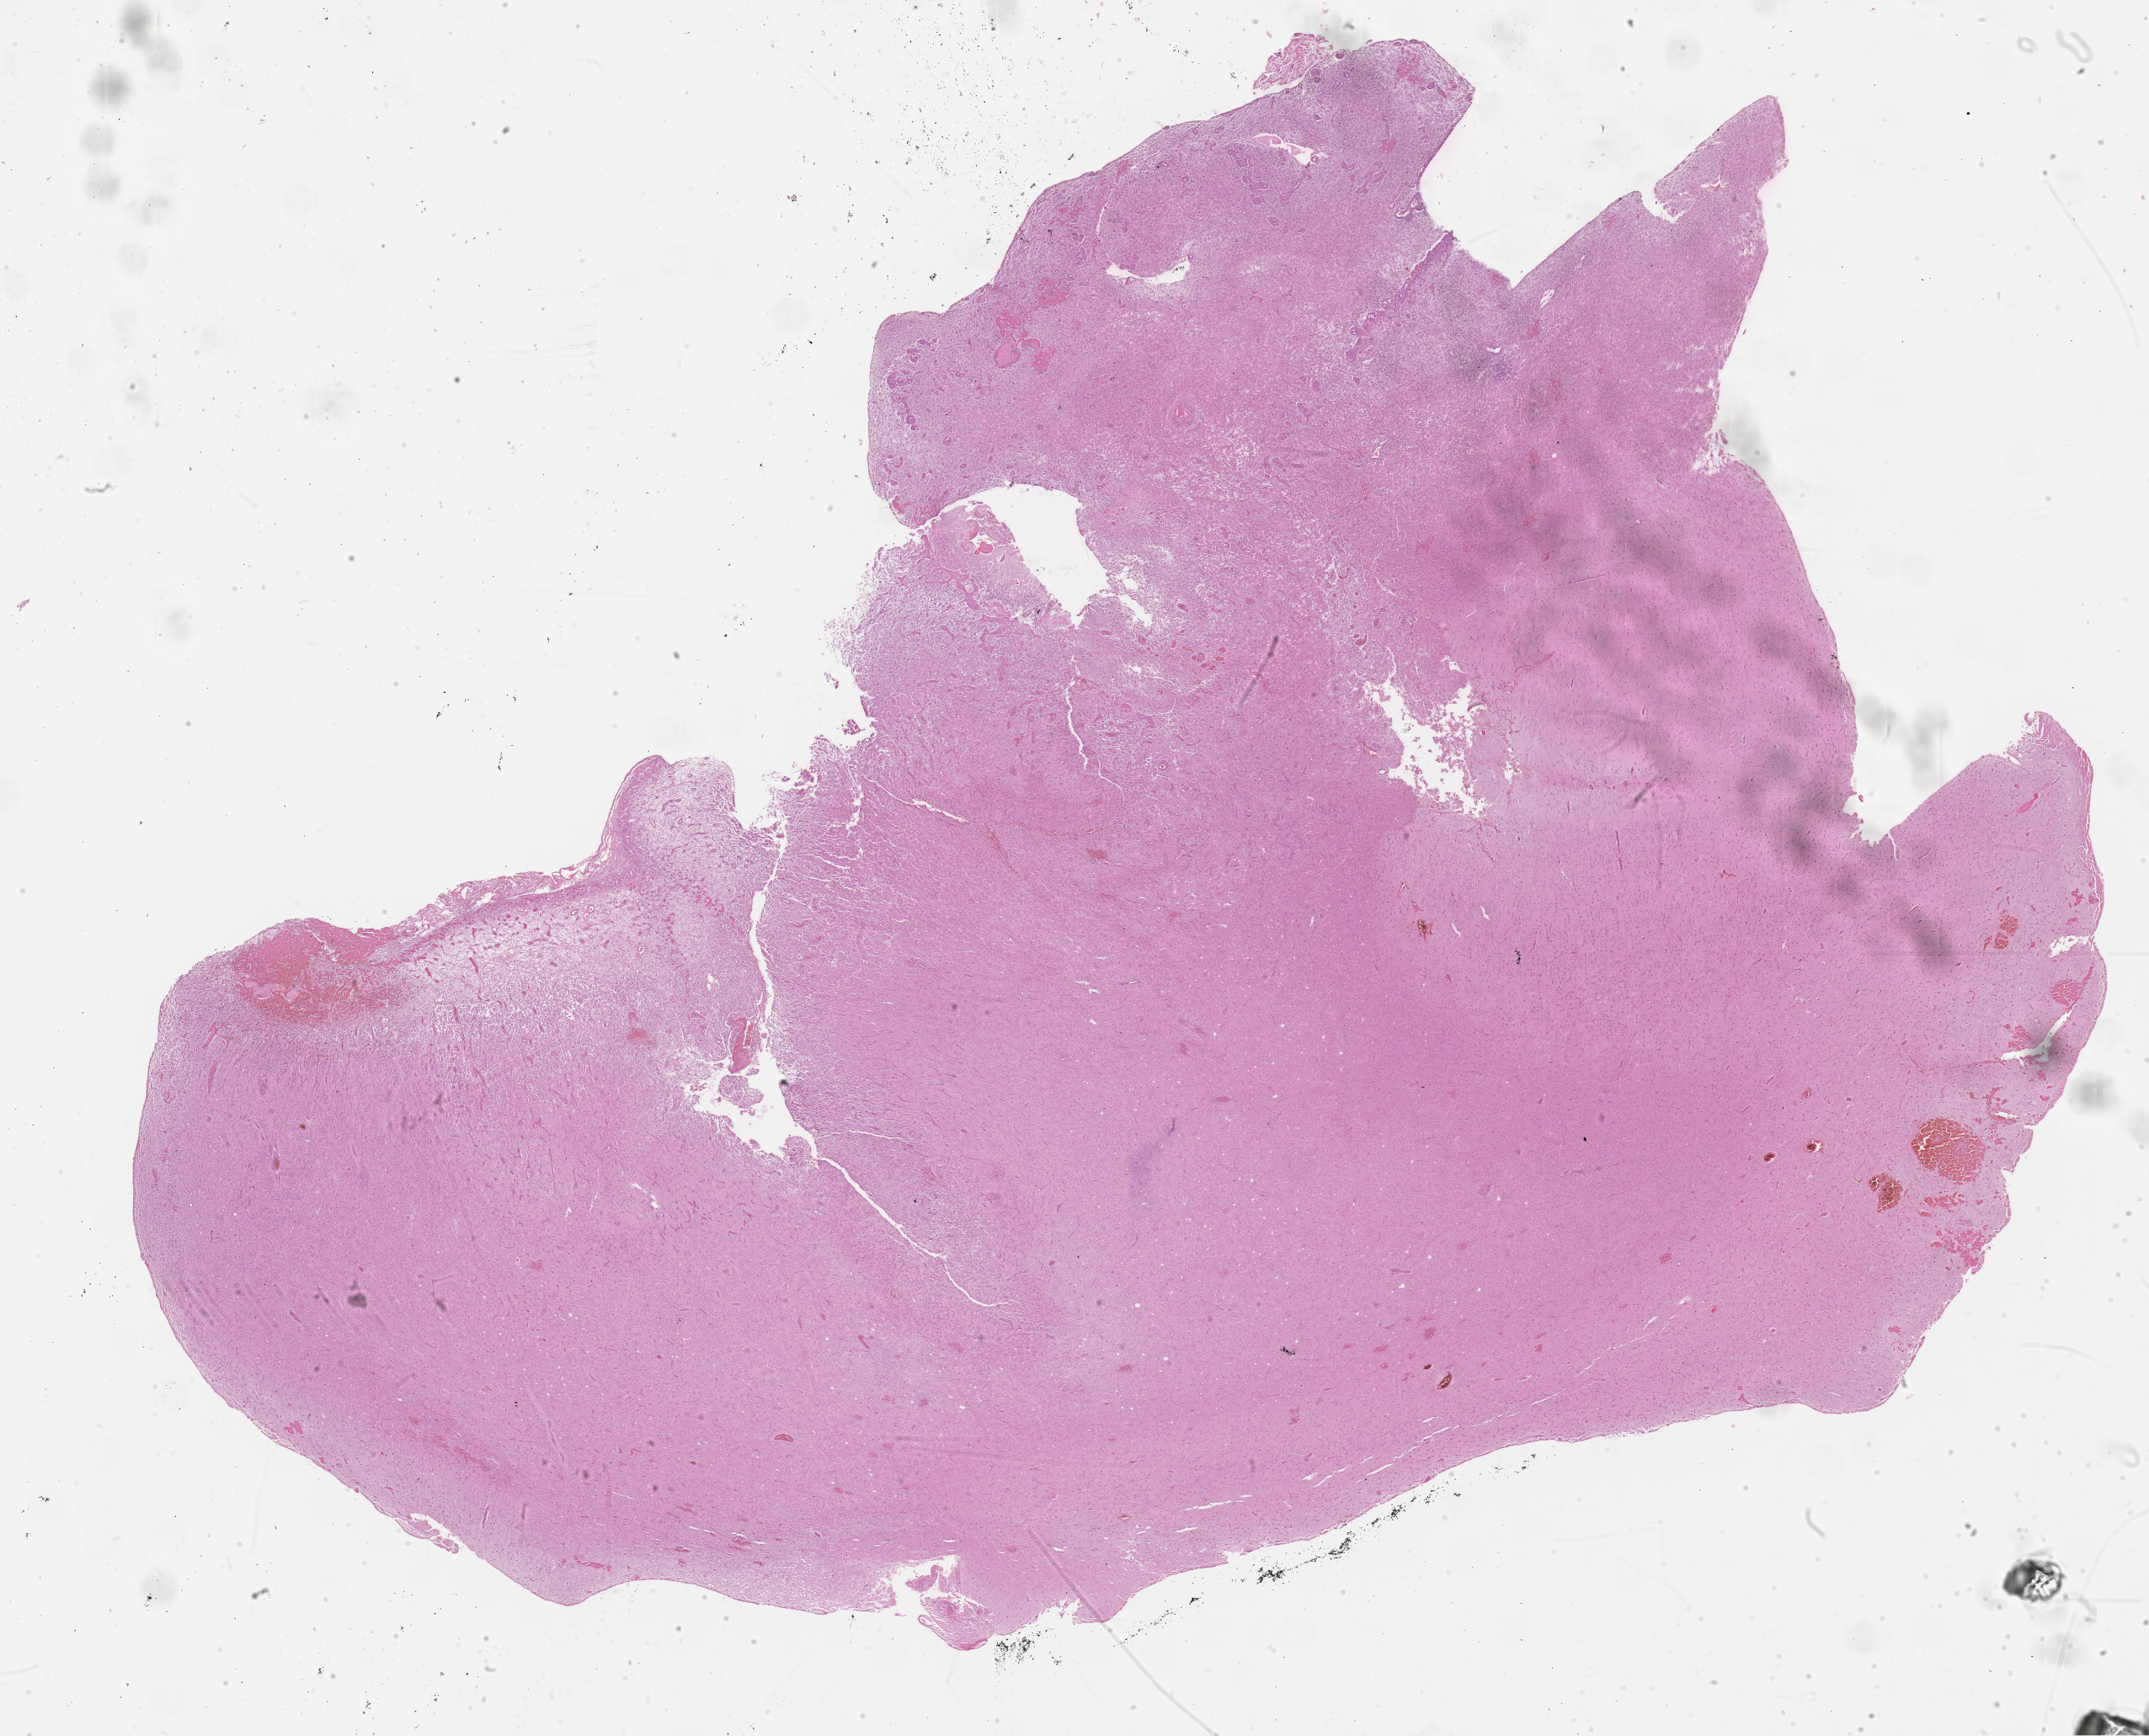
H&E whole-slide image, whole scanned area (about 20.7 x 16.7 mm, slide scanned at 40x) shown as a low-resolution overview. FFPE section. Sample: primary tumour, brain. Patient: male, age at initial diagnosis 53 years.
Diagnosis: Glioblastoma.